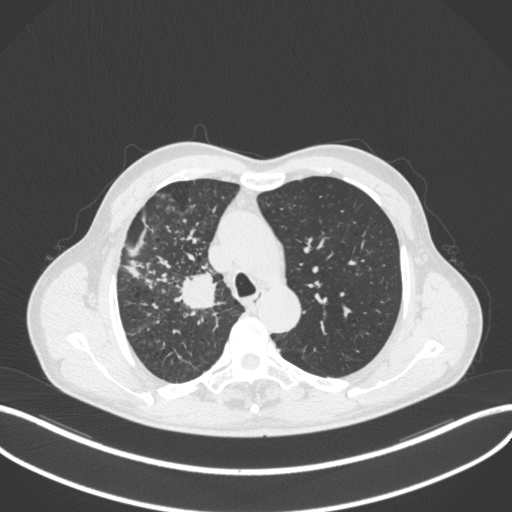
Chest CT, one axial slice. Position 348 of 490 along the scan axis. Reconstruction kernel B31f. 120 kVp. Lung window (W 1500 / L -600 HU). 1 mm slice thickness. 512 × 512 image matrix. Male patient, age 69 years. From the clinical record (not read from this slice): clinical TNM (as recorded): T2a N0 M0.
Annotated regions visible in this slice (bounding box drawn by a radiologist):
- lung tumour (recorded histology: adenocarcinoma): box from (x=172, y=273) to (x=223, y=317) px